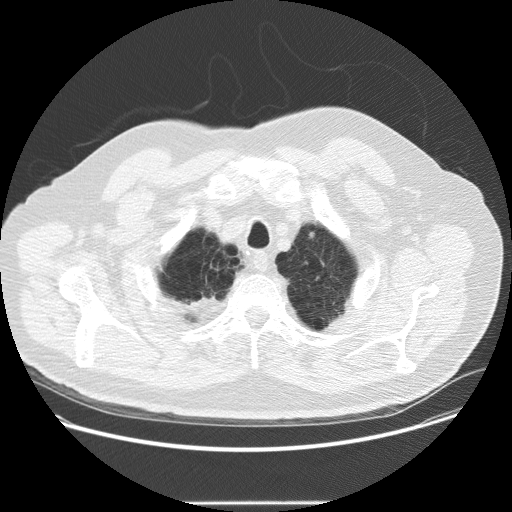
Chest CT (low-dose screening protocol), one axial image. Second annual screen. Lung window (W 1500 / L -600 HU). Standard (soft-tissue) reconstruction kernel (STANDARD). 120 kVp. 512 × 512 image matrix. Male participant, aged 64 years at enrolment.
Expert reader's lesion annotation, bounding box [x1, y1, x2, y2] px = [300, 224, 326, 249]. Screening reader's record for this exam (one nodule recorded; not confirmed to be the boxed lesion): non-calcified nodule or mass ≥4 mm, left upper lobe, 5 × 3 mm, smooth margins, soft tissue attenuation, pre-existing on the prior screen: no. Official screen result: positive, other.